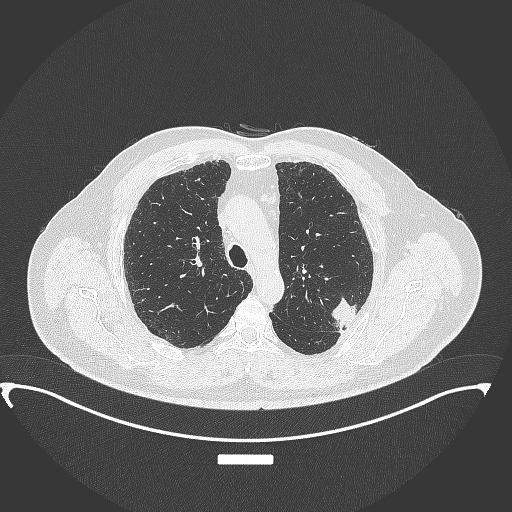
Chest CT, one axial slice; position 260 of 350 along the scan axis; reconstruction kernel B70f; 120 kVp; lung window (W 1500 / L -600 HU); 1 mm slice thickness; 512 × 512 image matrix. Male patient, age 64 years. From the clinical record (not read from this slice): clinical TNM (as recorded): T1c N1 M1.
Structures marked on this image (rectangle marked by the reading radiologist):
- lung tumour (recorded histology: adenocarcinoma): bounding box <329,294,362,332> (left, top, right, bottom; pixels)